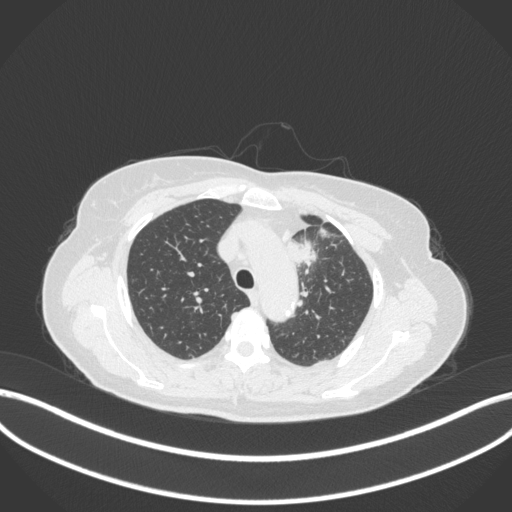
Chest CT, one axial slice. Position 254 of 368 along the scan axis. 120 kVp. Lung window (W 1500 / L -600 HU). 1 mm slice thickness. 512 × 512 image matrix, field of view 400 × 400 mm. Female patient, age 65 years. From the clinical record (not read from this slice): clinical TNM (as recorded): T2a N0 M0; histopathological grade: G2-3.
Annotated regions visible in this slice (rectangle marked by the reading radiologist):
- lung tumour (recorded histology: adenocarcinoma): bounding box <282,236,319,270> (left, top, right, bottom; pixels)